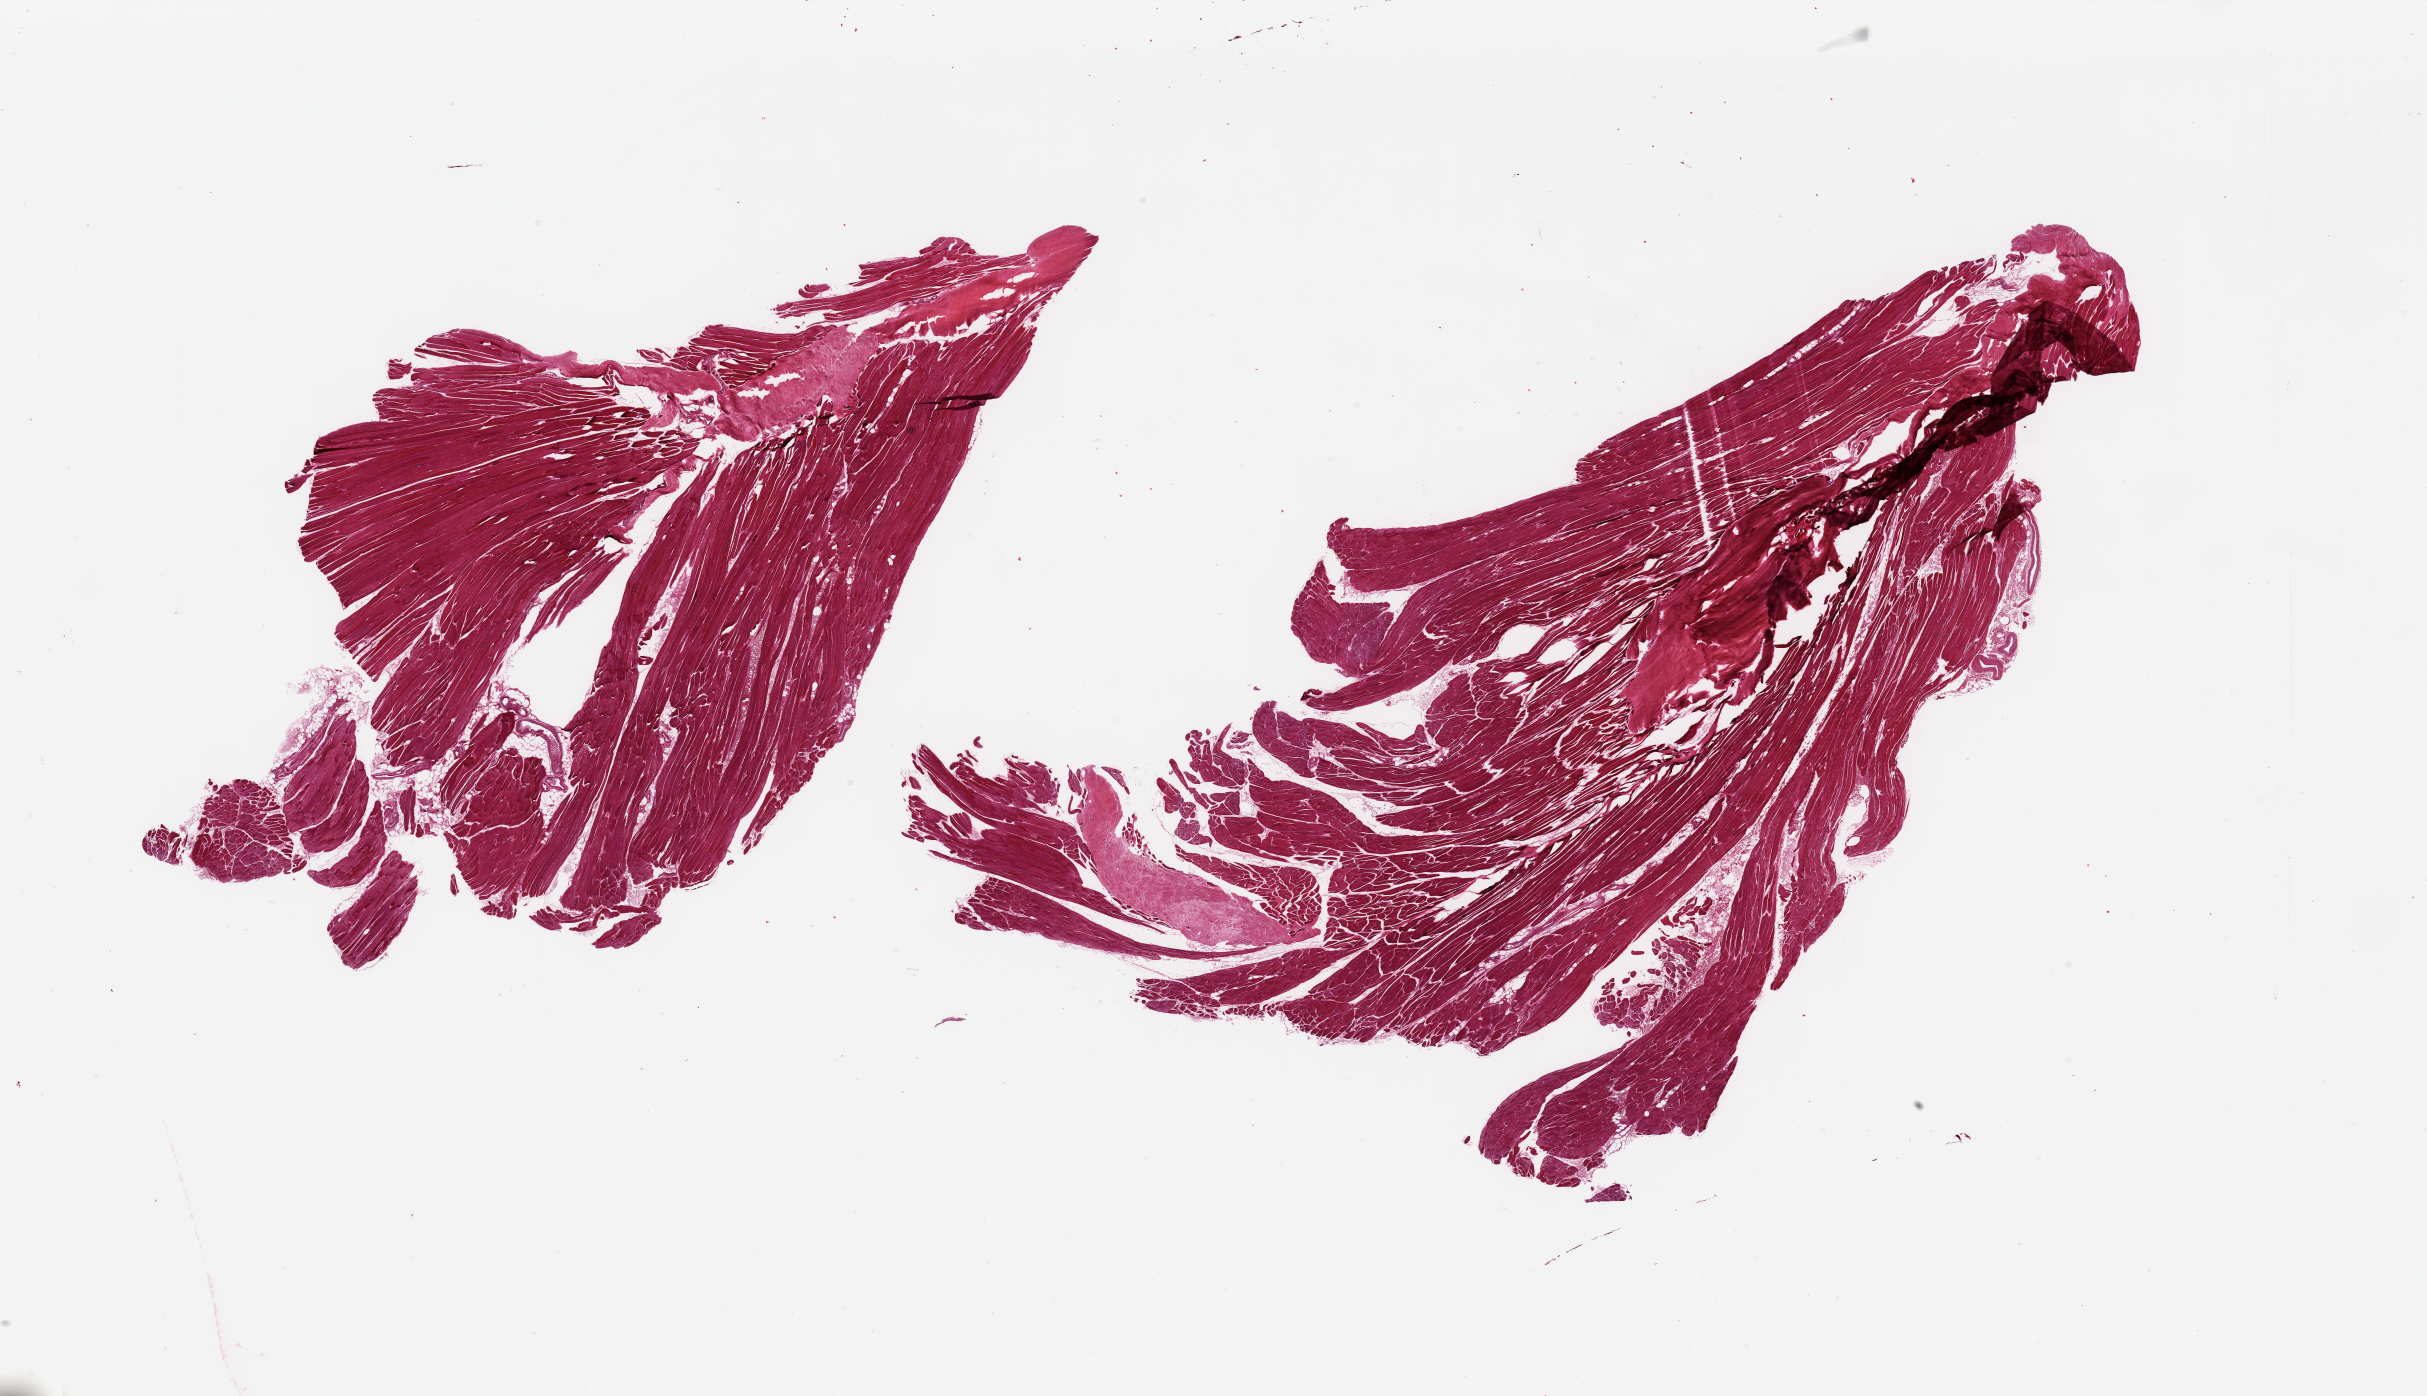
Whole-slide image, H&E stain, brightfield, low-resolution overview of the scanned area, about 38.4 x 22.1 mm (slide scanned at 20x), PAXgene-fixed paraffin-embedded (PFPE) section, target tissue: skeletal muscle, tissue donor sample. Donor: male.
Reviewer comment on this tissue sample: 2 partly fragmented pieces; 3 foci of dense fibrous tissue c/w tendon or fascia.